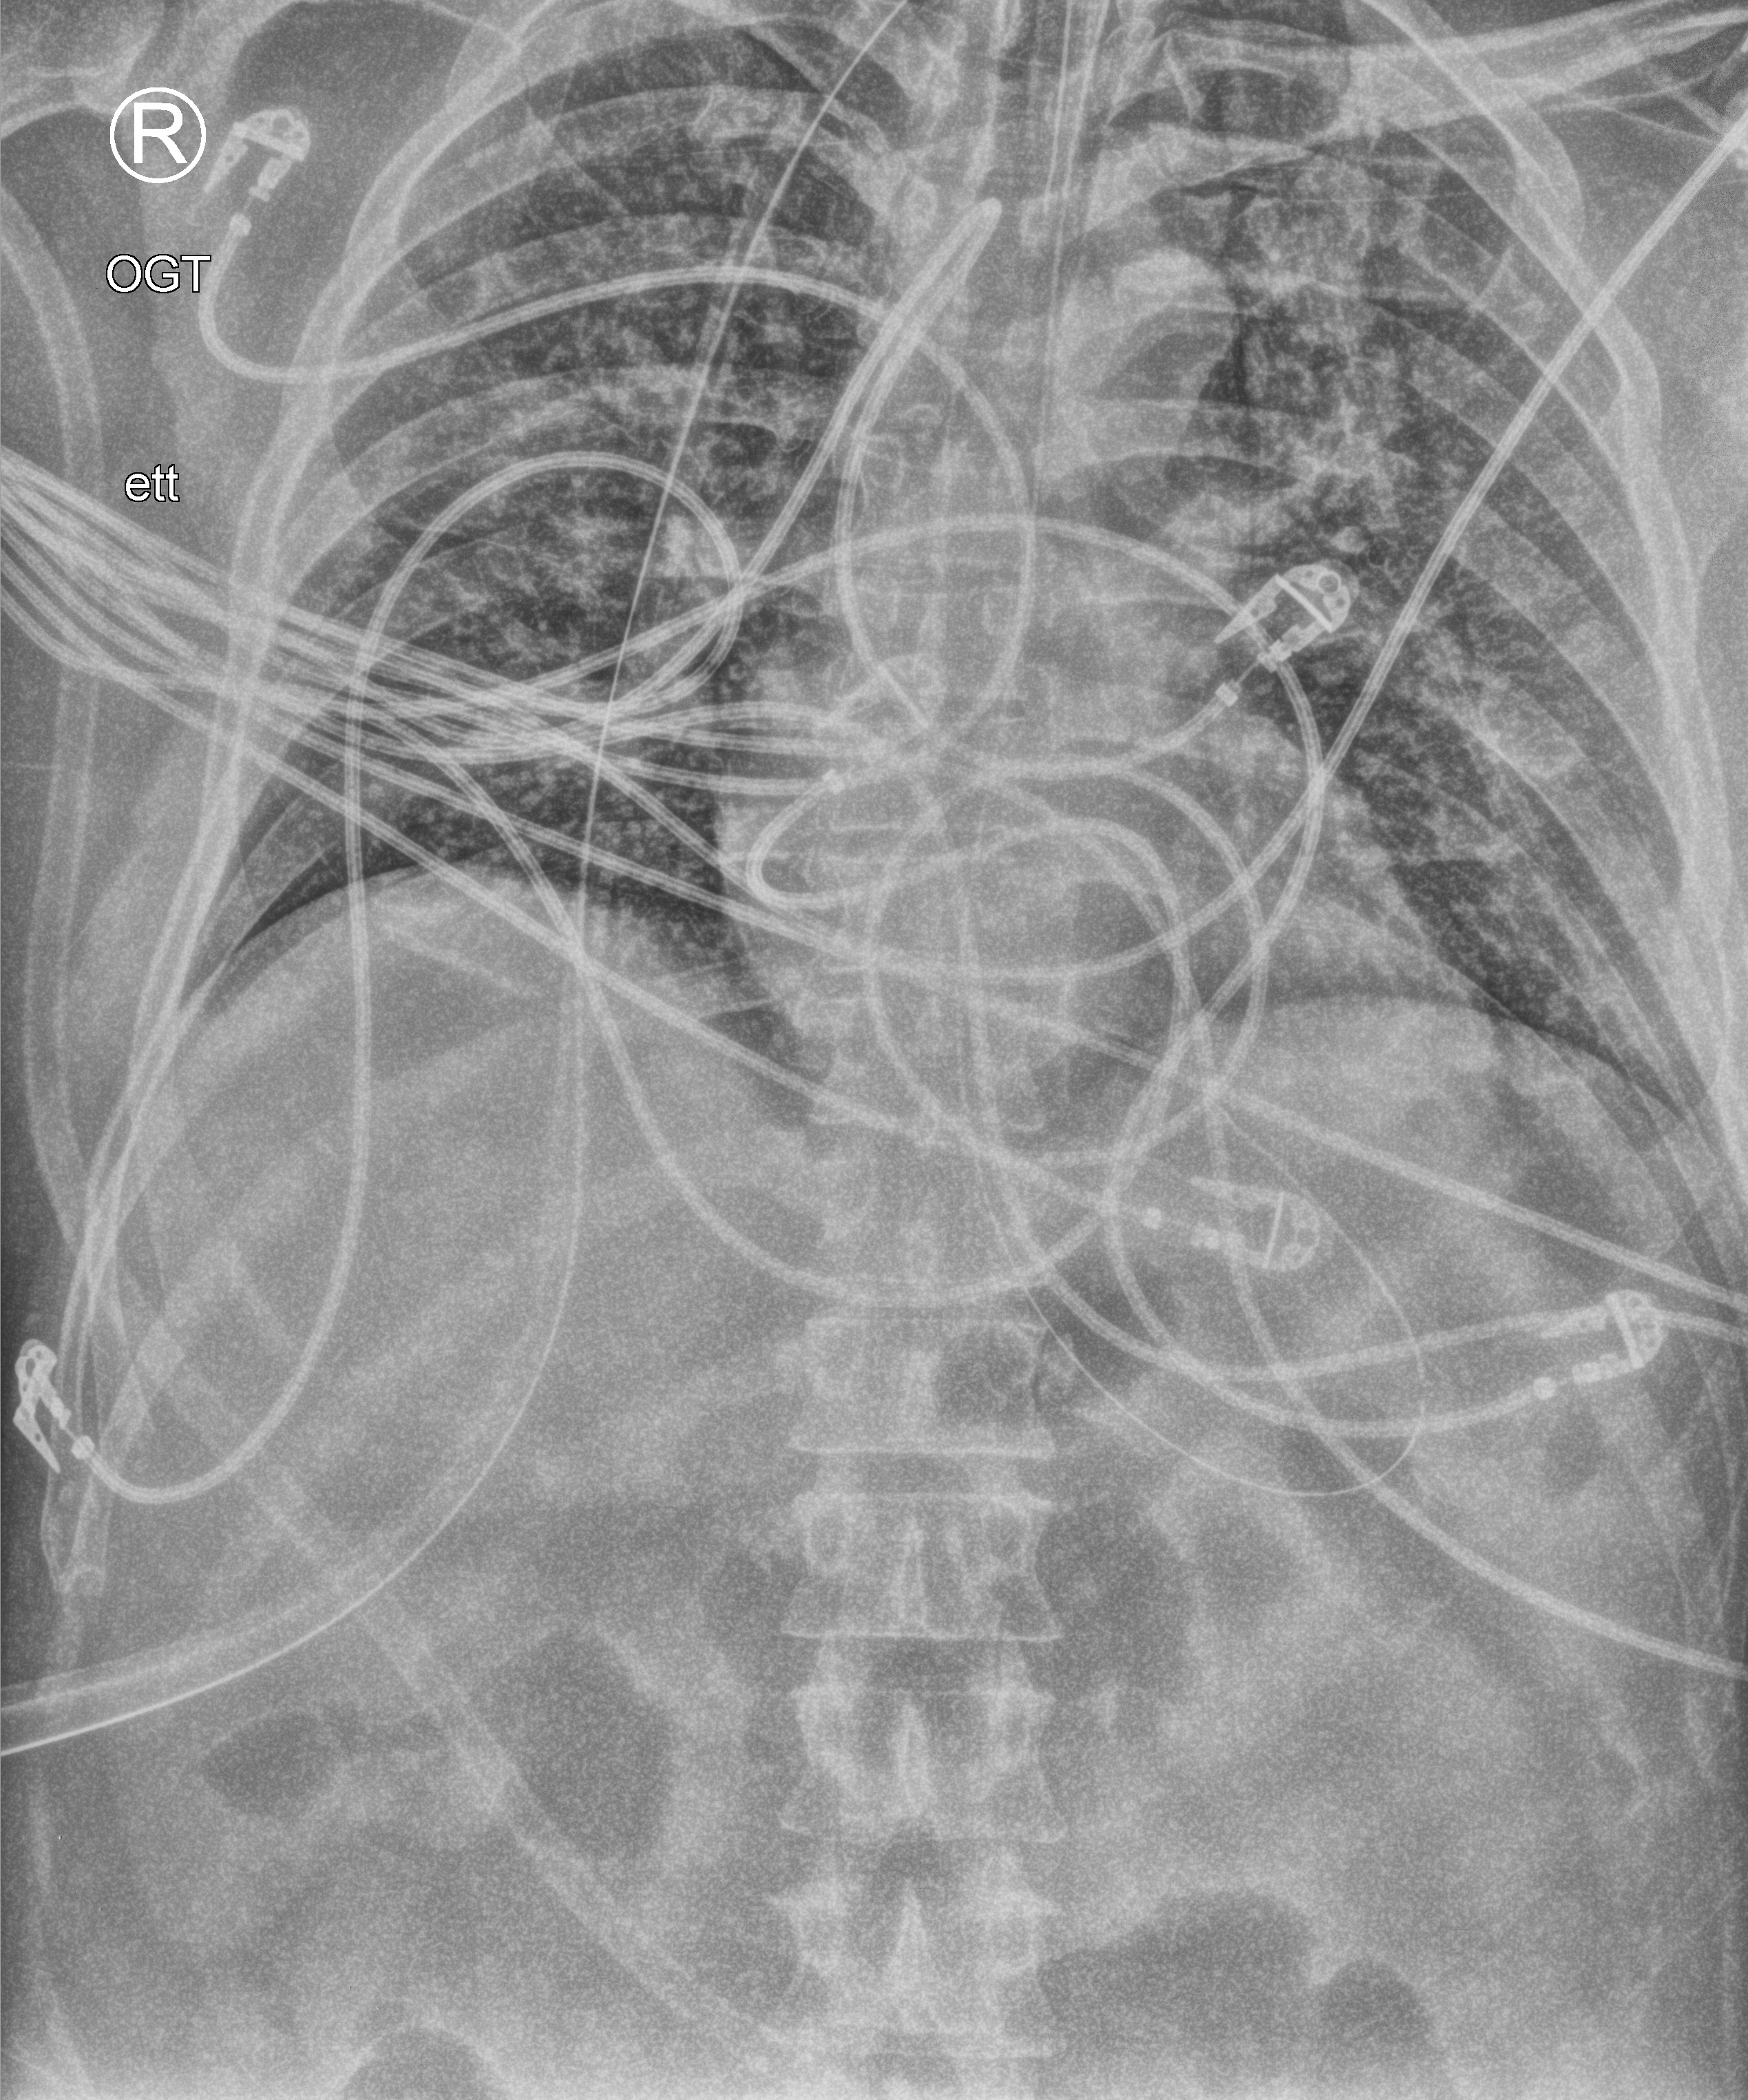
Bedside chest radiograph (computed radiography). Male patient hospitalised with COVID-19, age 18–59 years.
Hospital-stay facts (about this admission, not read from this image; timing relative to this image not recorded): mechanically ventilated during this hospital stay: yes; length of hospital stay: 10 days; admitted to intensive care during this hospital stay: yes.